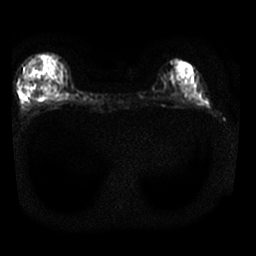
Breast MRI, one axial slice. Slice 10 of 25 in the series (ordered by position). Diffusion-weighted series; image 2 of 4 stored at this slice position (different b-values; order by instance number). 1.5 T. 4 mm slice thickness. 256 × 256 image matrix, field of view 310 × 310 mm. Female patient.
Structures marked on this image (manually delineated by an expert):
- tumour on diffusion-weighted imaging: box from (x=47, y=94) to (x=52, y=96) px